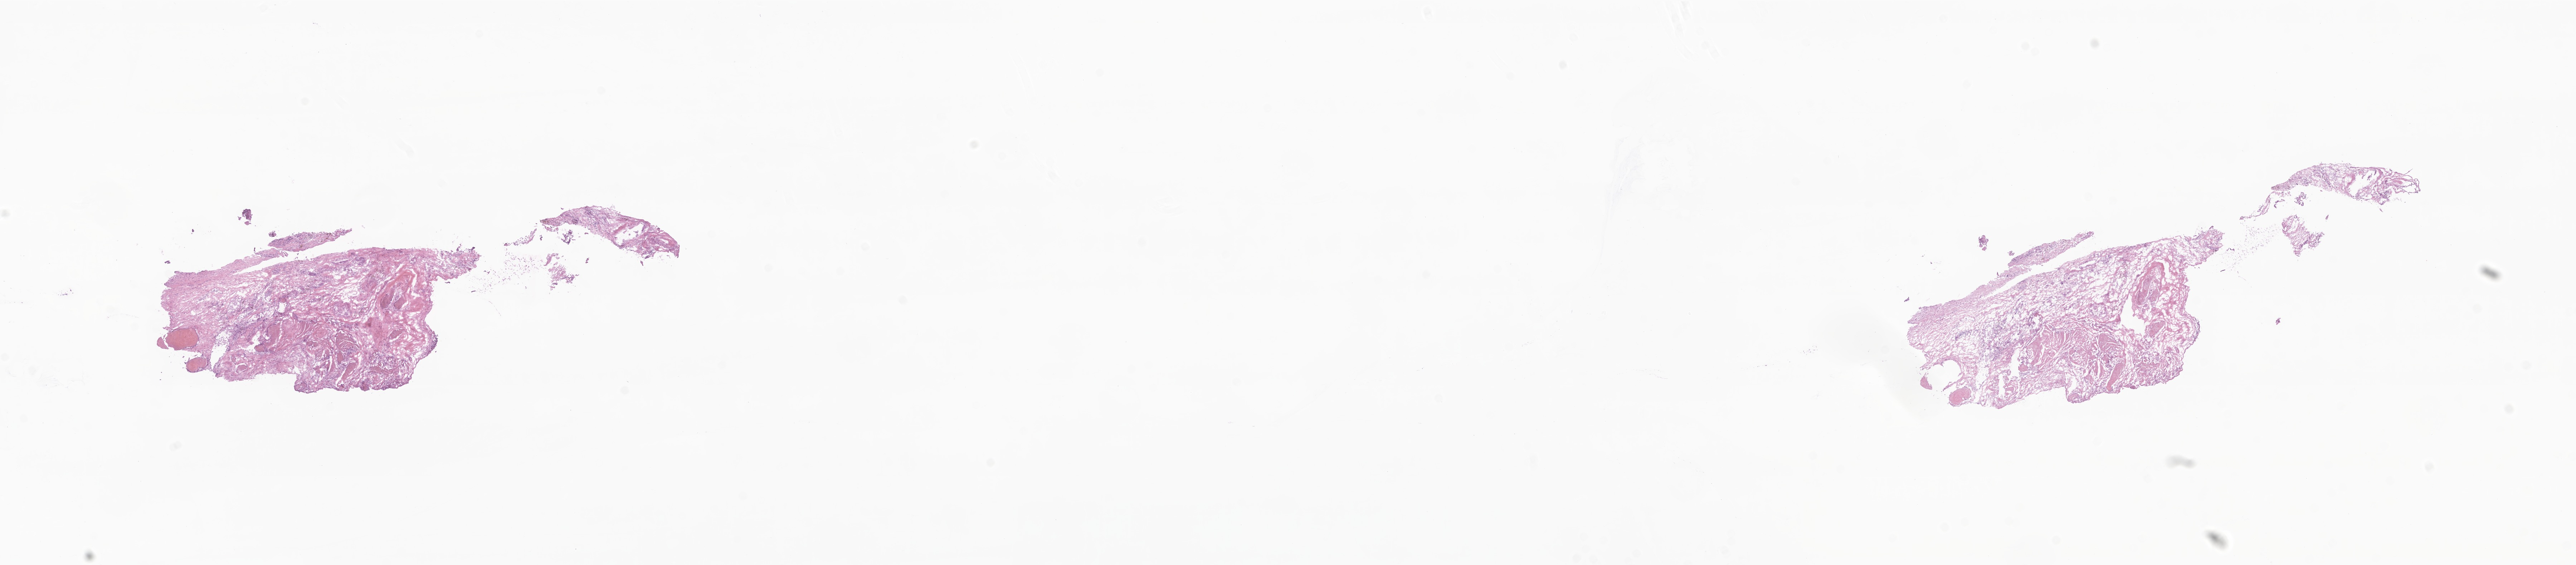
Digitized H&E-stained section of tumor tissue from the brain — shown as a low-resolution overview of the whole scanned area (about 30.4 x 6.7 mm); cryosection (OCT / tissue freezing medium). Male patient, age 111 months (9 years 3 months).
- recorded diagnosis: Craniopharyngioma, adamantinomatous